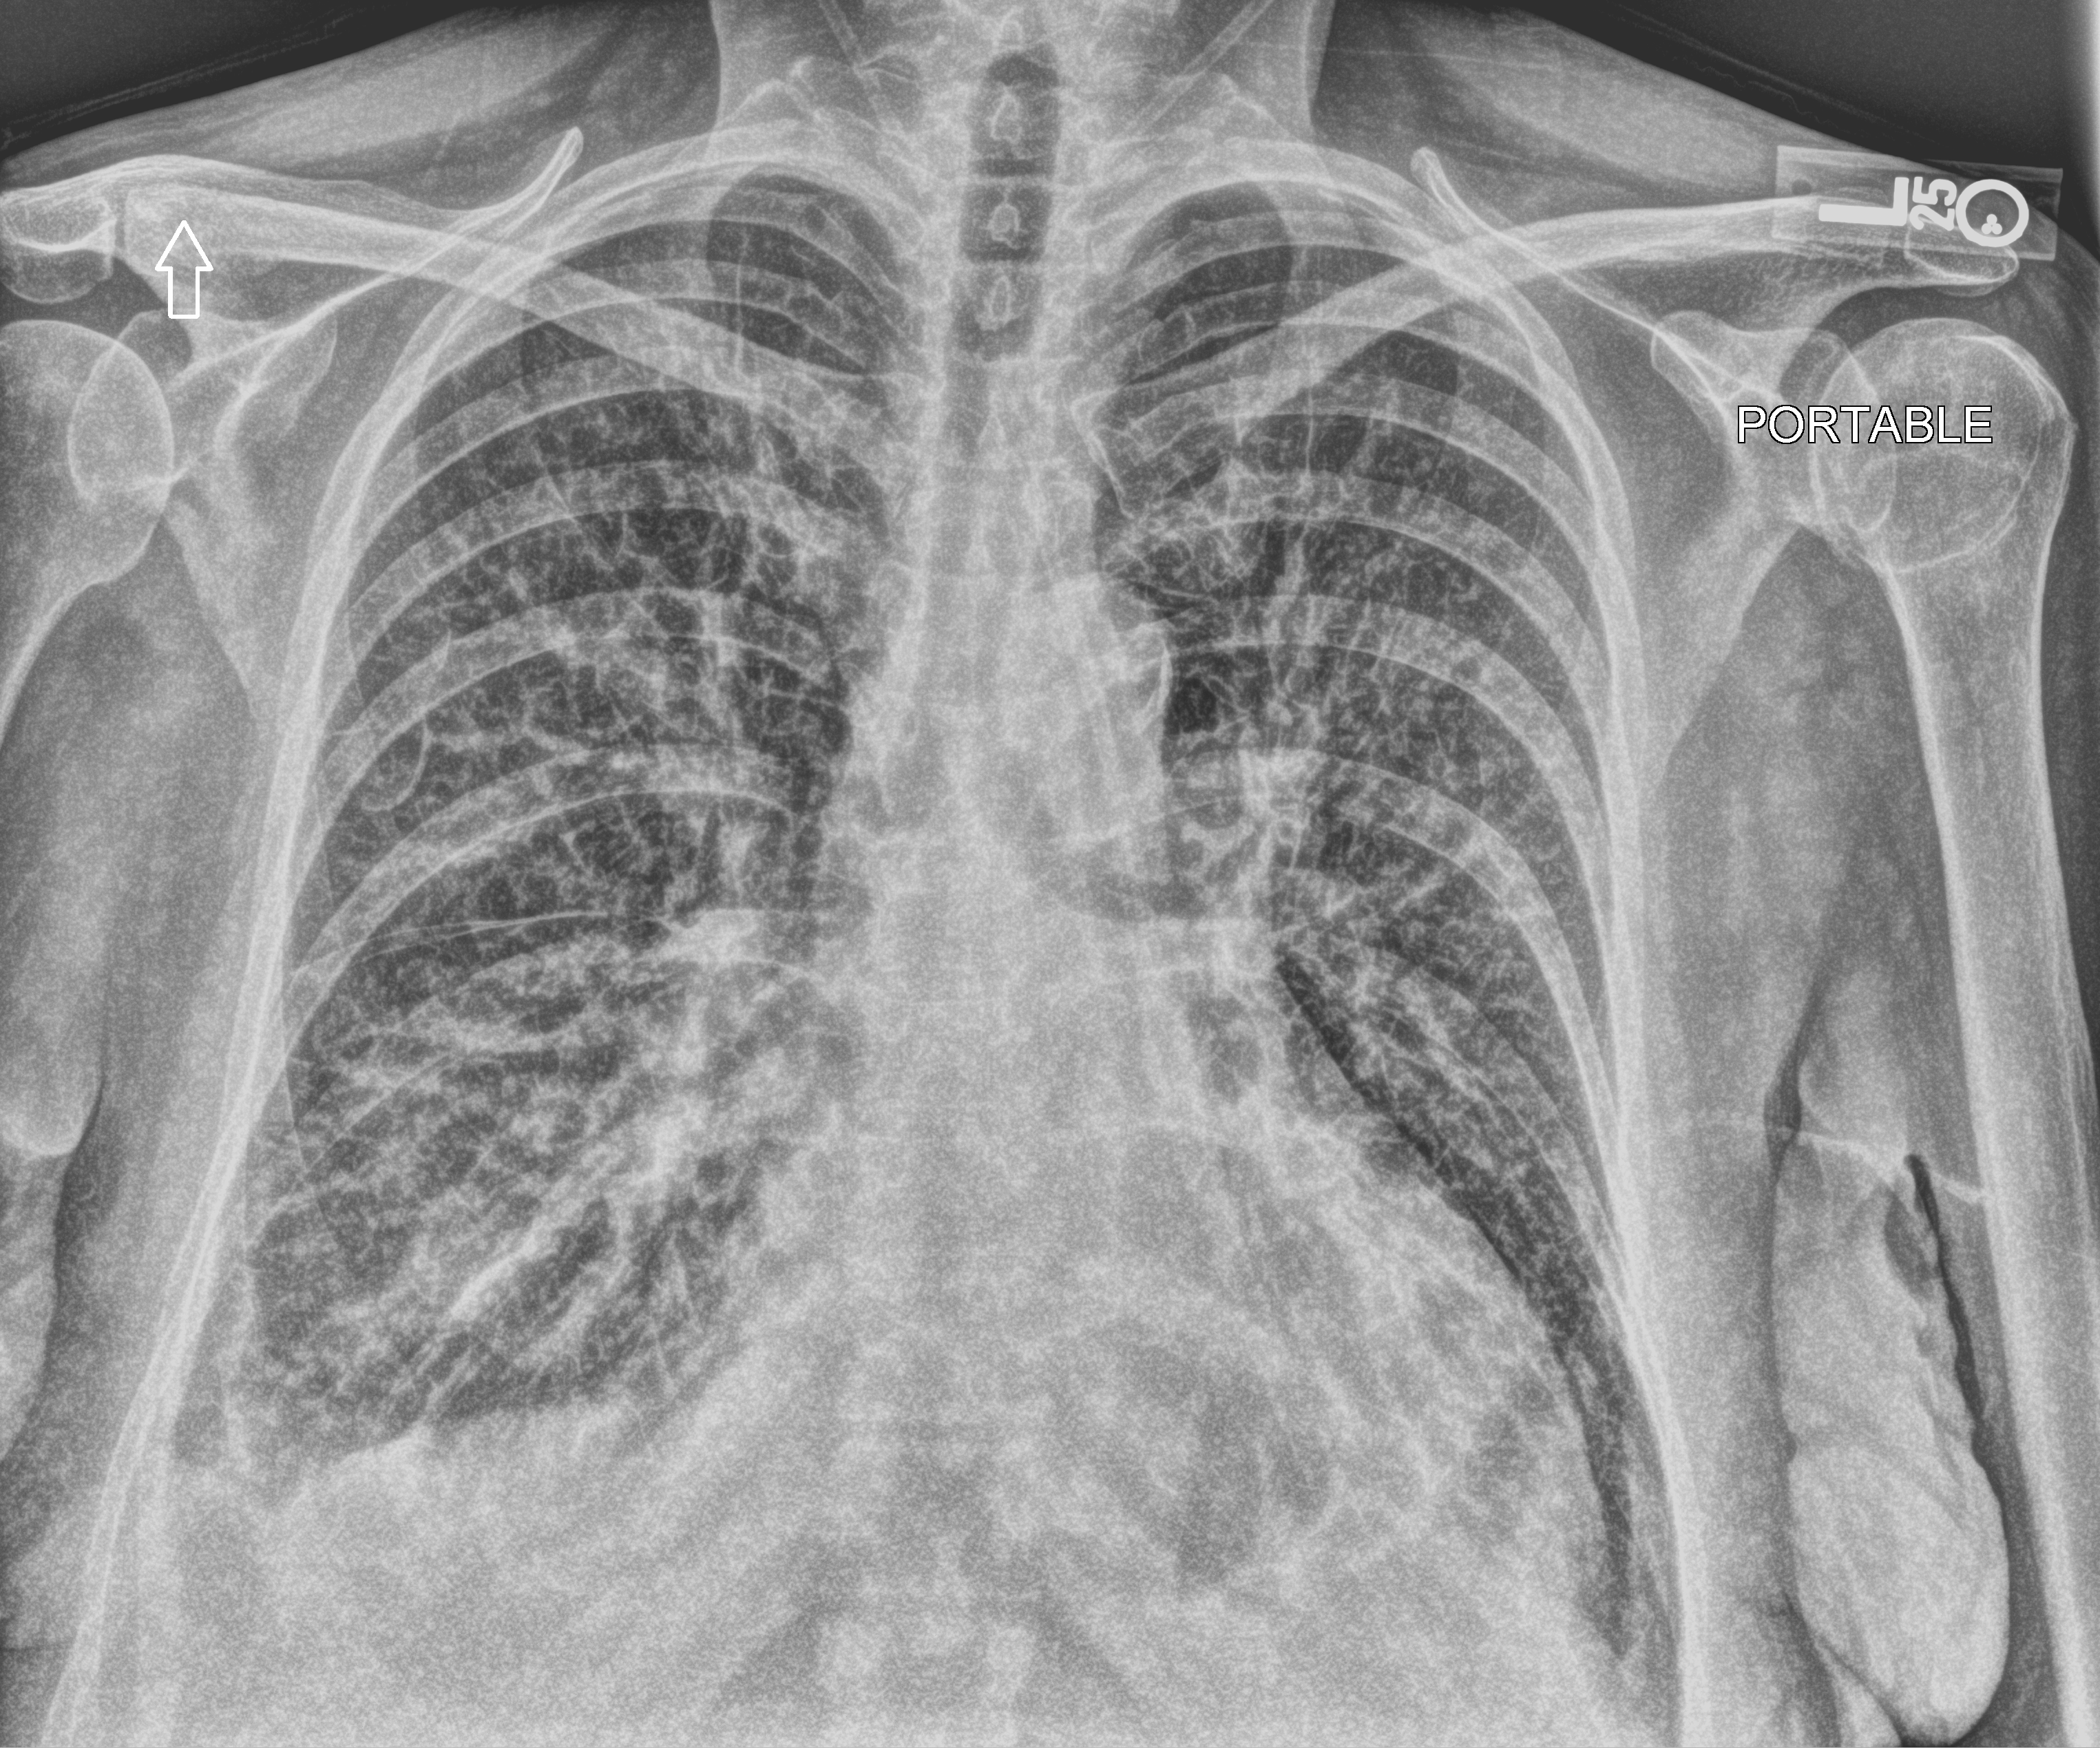
Portable chest radiograph. Patient hospitalised with COVID-19; female, aged 18–59 years.
Admission-level facts for this patient (not findings on this image; timing relative to this image not recorded):
- admitted to intensive care during this hospital stay: no
- length of hospital stay: 11 days
- mechanically ventilated during this hospital stay: no